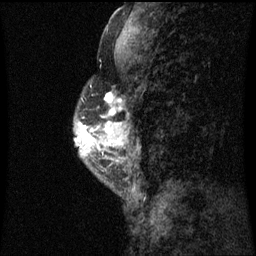
Breast MRI (dynamic contrast-enhanced), one sagittal slice. Slice 22 of 60 in the series (ordered by position). Dynamic contrast-enhanced series, image 2 of 3 at this slice position (ordered by acquisition). 1.5 T. TE 4.2 ms, TR 8.9 ms. 2 mm slice thickness. 256 × 256 image matrix, field of view 200 × 200 mm. Patient: female, 50 years. Case-level facts recorded for this patient, not image findings: setting: breast cancer imaged before/during neoadjuvant chemotherapy; receptor status: triple-negative.
Annotated regions visible in this slice (semi-automatically segmented with operator editing):
- analysis volume of interest (the breast-tissue region the enhancement analysis was run in; not a lesion): box from (x=75, y=86) to (x=116, y=169) px
- tumour enhancement mask (voxels above the 70 % enhancement threshold inside the analysis volume of interest): (x=78, y=92)–(x=116, y=151)